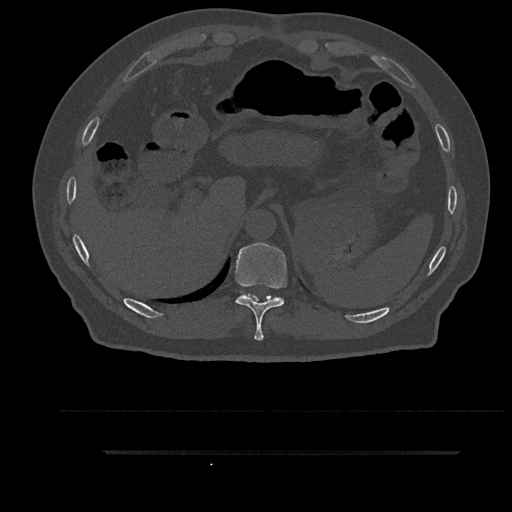
CT including the spine, one axial slice; position 353 of 797 along the scan axis; reconstruction kernel Br40s/3; bone window (W 1800 / L 400 HU); 0.5 mm slice thickness; 512 × 512 image matrix, field of view 432 × 432 mm. Male patient, age 63 years. Case-level facts recorded for this patient, not image findings: primary cancer: renal.
Outlined on this slice (semi-automatically segmented with operator editing):
- T10 vertebra: bounding box <235,242,288,341> (left, top, right, bottom; pixels)
- T11 vertebra: <241,292,279,299>